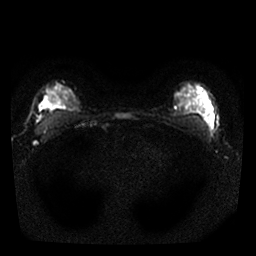
Breast MRI, one axial slice. Position 20 of 25 along the scan axis. Diffusion-weighted series; image 2 of 4 stored at this slice position (different b-values; order by instance number). 1.5 T. 256 × 256 image matrix, field of view 290 × 290 mm. Female patient.
Annotated regions visible in this slice (manually delineated by an expert):
- tumour on diffusion-weighted imaging: bounding box [x1, y1, x2, y2] px = [38, 90, 61, 110]